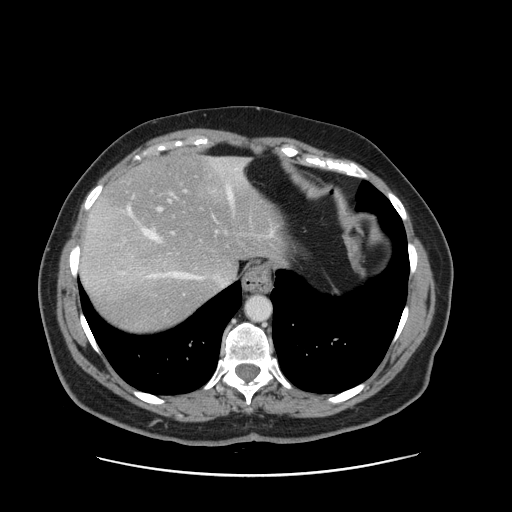
Contrast-enhanced abdominal CT, one axial slice. Slice 124 of 161 in the series (ordered by position). Intravenous contrast given. Soft-tissue window (W 400 / L 40 HU). 2.5 mm slice thickness. 512 × 512 image matrix. Female patient, age 62 years. Case-level facts recorded for this patient, not image findings: diagnosis: colorectal cancer liver metastases, imaged before liver resection; multiple liver metastases: no; largest metastasis: 2.5 cm; disease in both lobes: no.
Structures marked on this image (expert manual segmentation):
- hepatic veins: bounding box [x1, y1, x2, y2] px = [120, 160, 245, 285]
- liver: [81, 157, 286, 331]
- planned liver remnant (the part of the liver to remain after resection): [96, 157, 285, 279]
- portal vein (with intrahepatic branches): [158, 189, 274, 238]